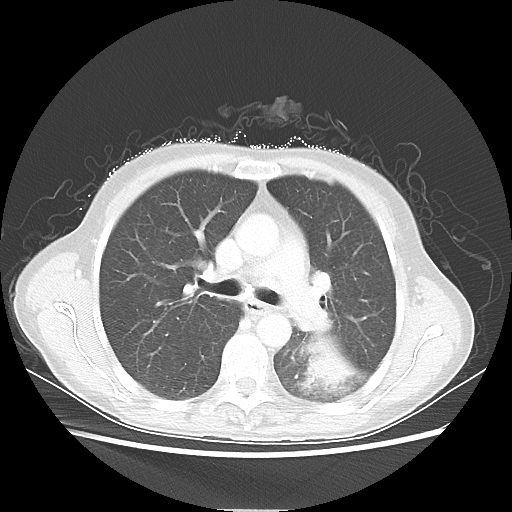
Chest CT, one axial slice; reconstruction kernel LUNG; 80 kVp; lung window (W 1500 / L -600 HU); 5 mm slice thickness; 512 × 512 image matrix. Female patient, age 53 years. From the clinical record (not read from this slice): clinical TNM (as recorded): T3 N0 M0.
Outlined on this slice (bounding box drawn by a radiologist):
- lung tumour (recorded histology: adenocarcinoma): bounding box <295,333,366,395> (left, top, right, bottom; pixels)